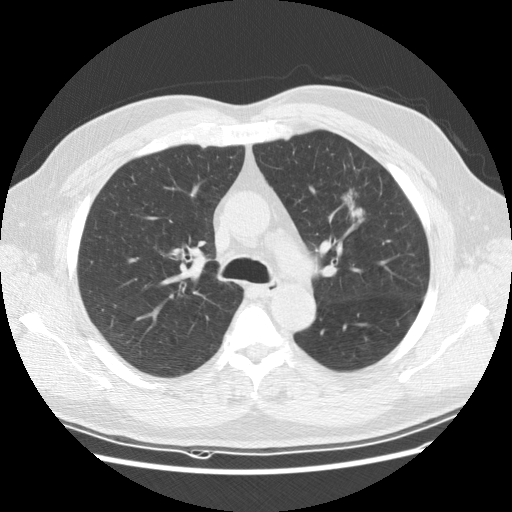
Axial slice from a low-dose chest CT screening exam; first (baseline) screen; lung window (W 1500 / L -600 HU); 2.5 mm slice thickness. Male, age 65 years at enrolment. Current smoker at enrolment.
Lesion marked by an expert reader, bounding box [x1, y1, x2, y2] px = [321, 178, 384, 236]. The screening reader recorded 2 non-calcified nodules or masses ≥4 mm on this exam; which of them this box marks is not recorded. Official screen result: positive, change unspecified: nodule(s) >= 4 mm or enlarging nodule(s), mass(es), or other non-specific abnormalities suspicious for lung cancer. Lung cancer was diagnosed 488 days after this screen (after the second annual screen): carcinoma, NOS, left upper lobe, poorly differentiated (G3), stage IIIA (AJCC 6th edition), 25 mm at pathology.